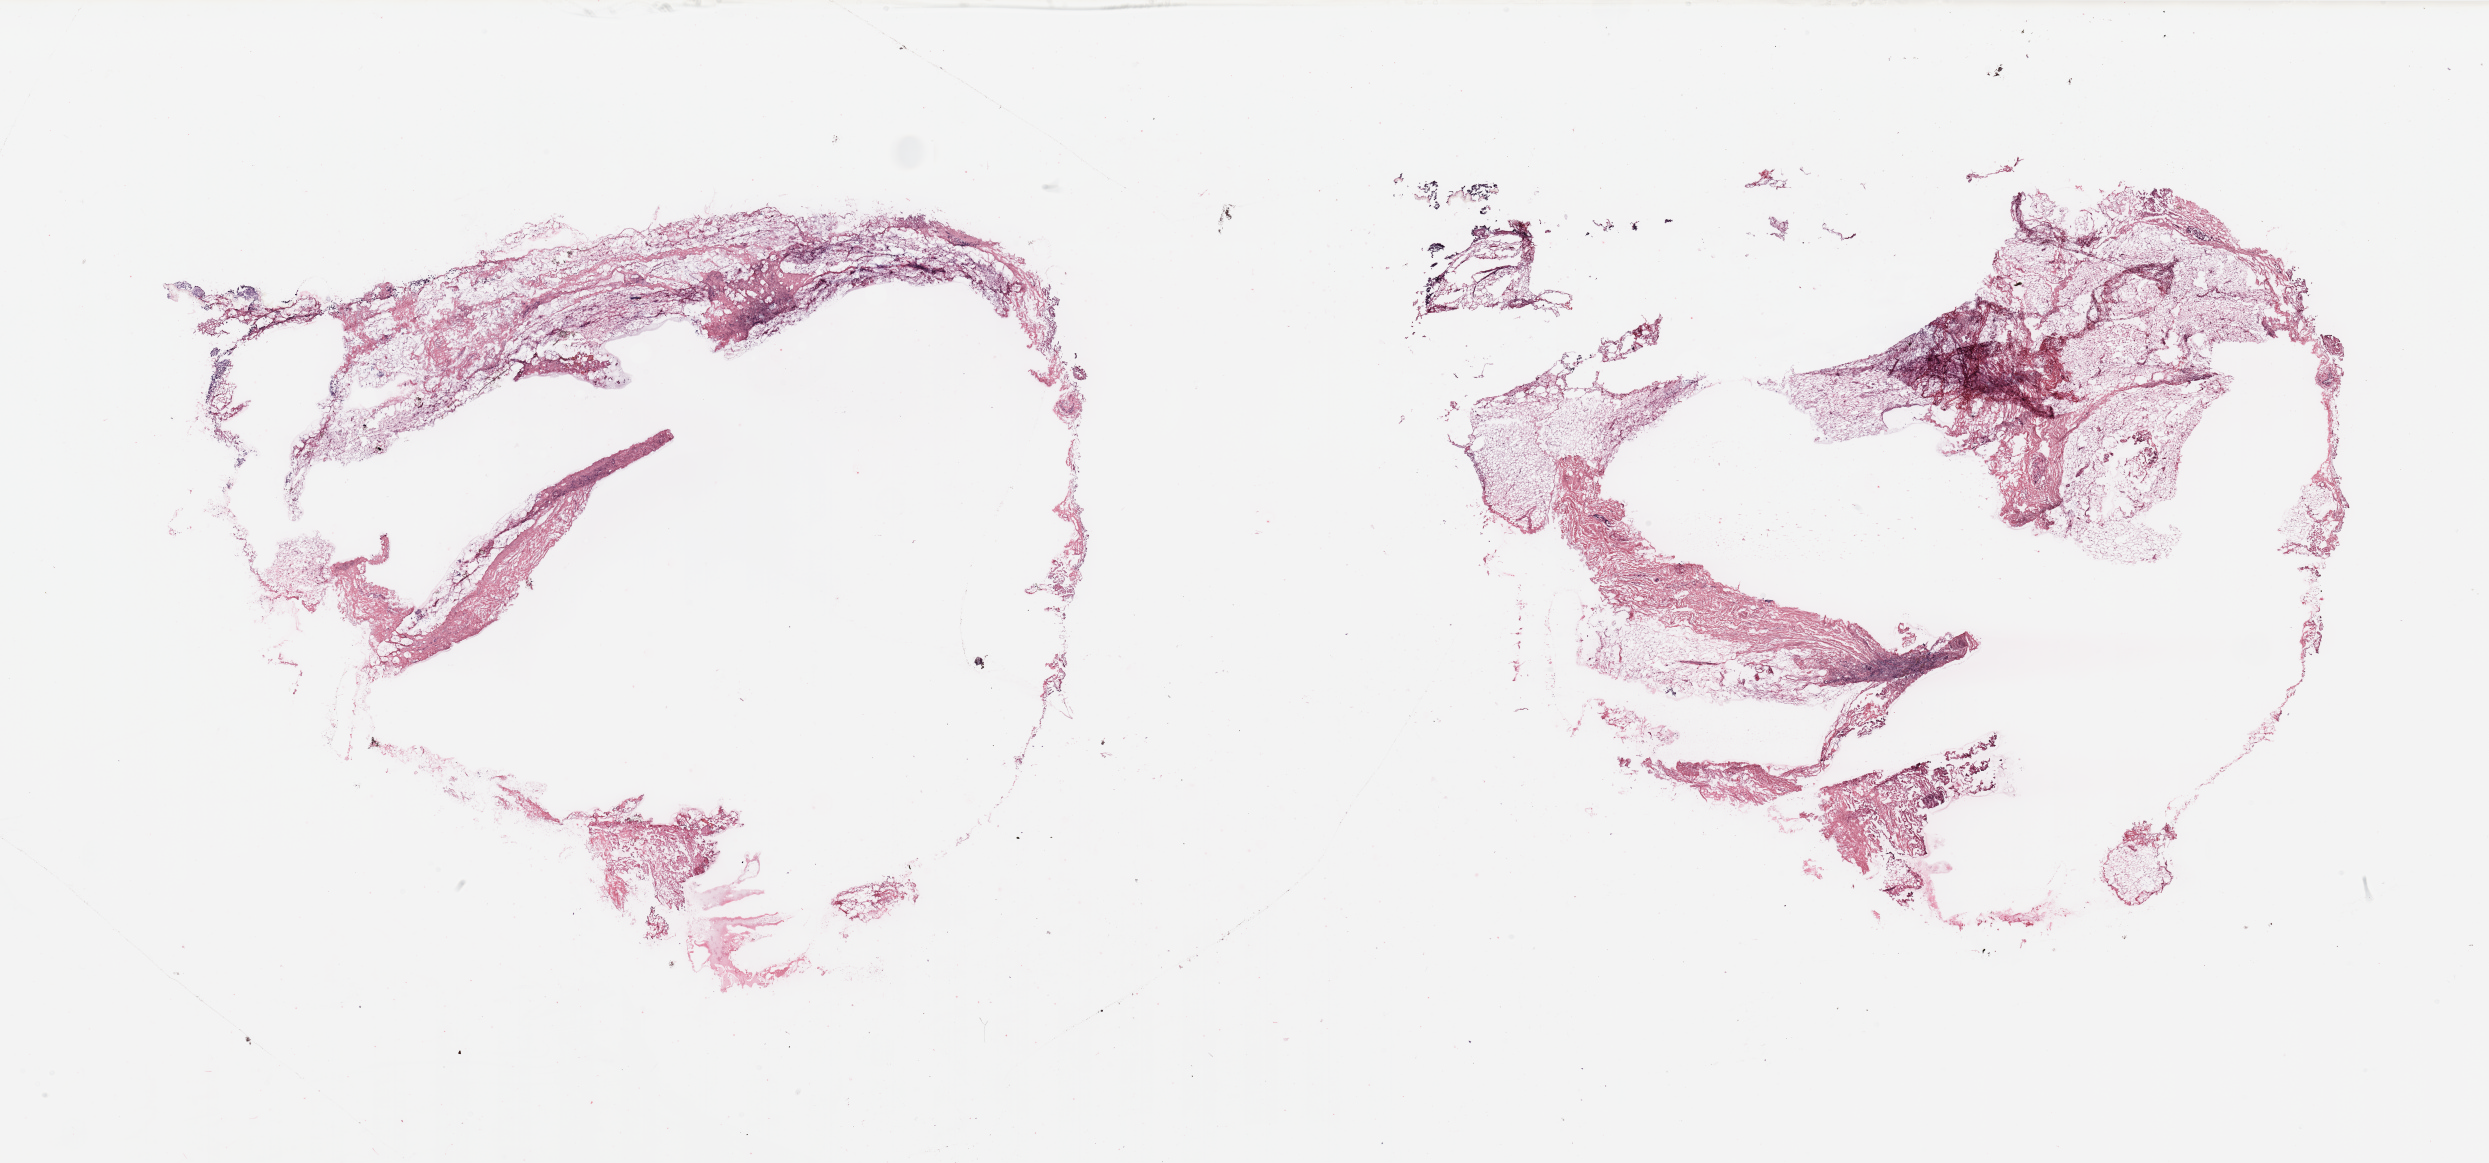
Whole-slide histology image, Hematoxylin and eosin (H&E) stained — a low-resolution overview of the entire scanned area, about 39.4 x 18.4 mm (acquisition: 20x scan); breast, tumour tissue. Female, 80 y/o.
• AJCC pathologic stage: IIA
• histologic diagnosis: Infiltrating duct carcinoma, NOS